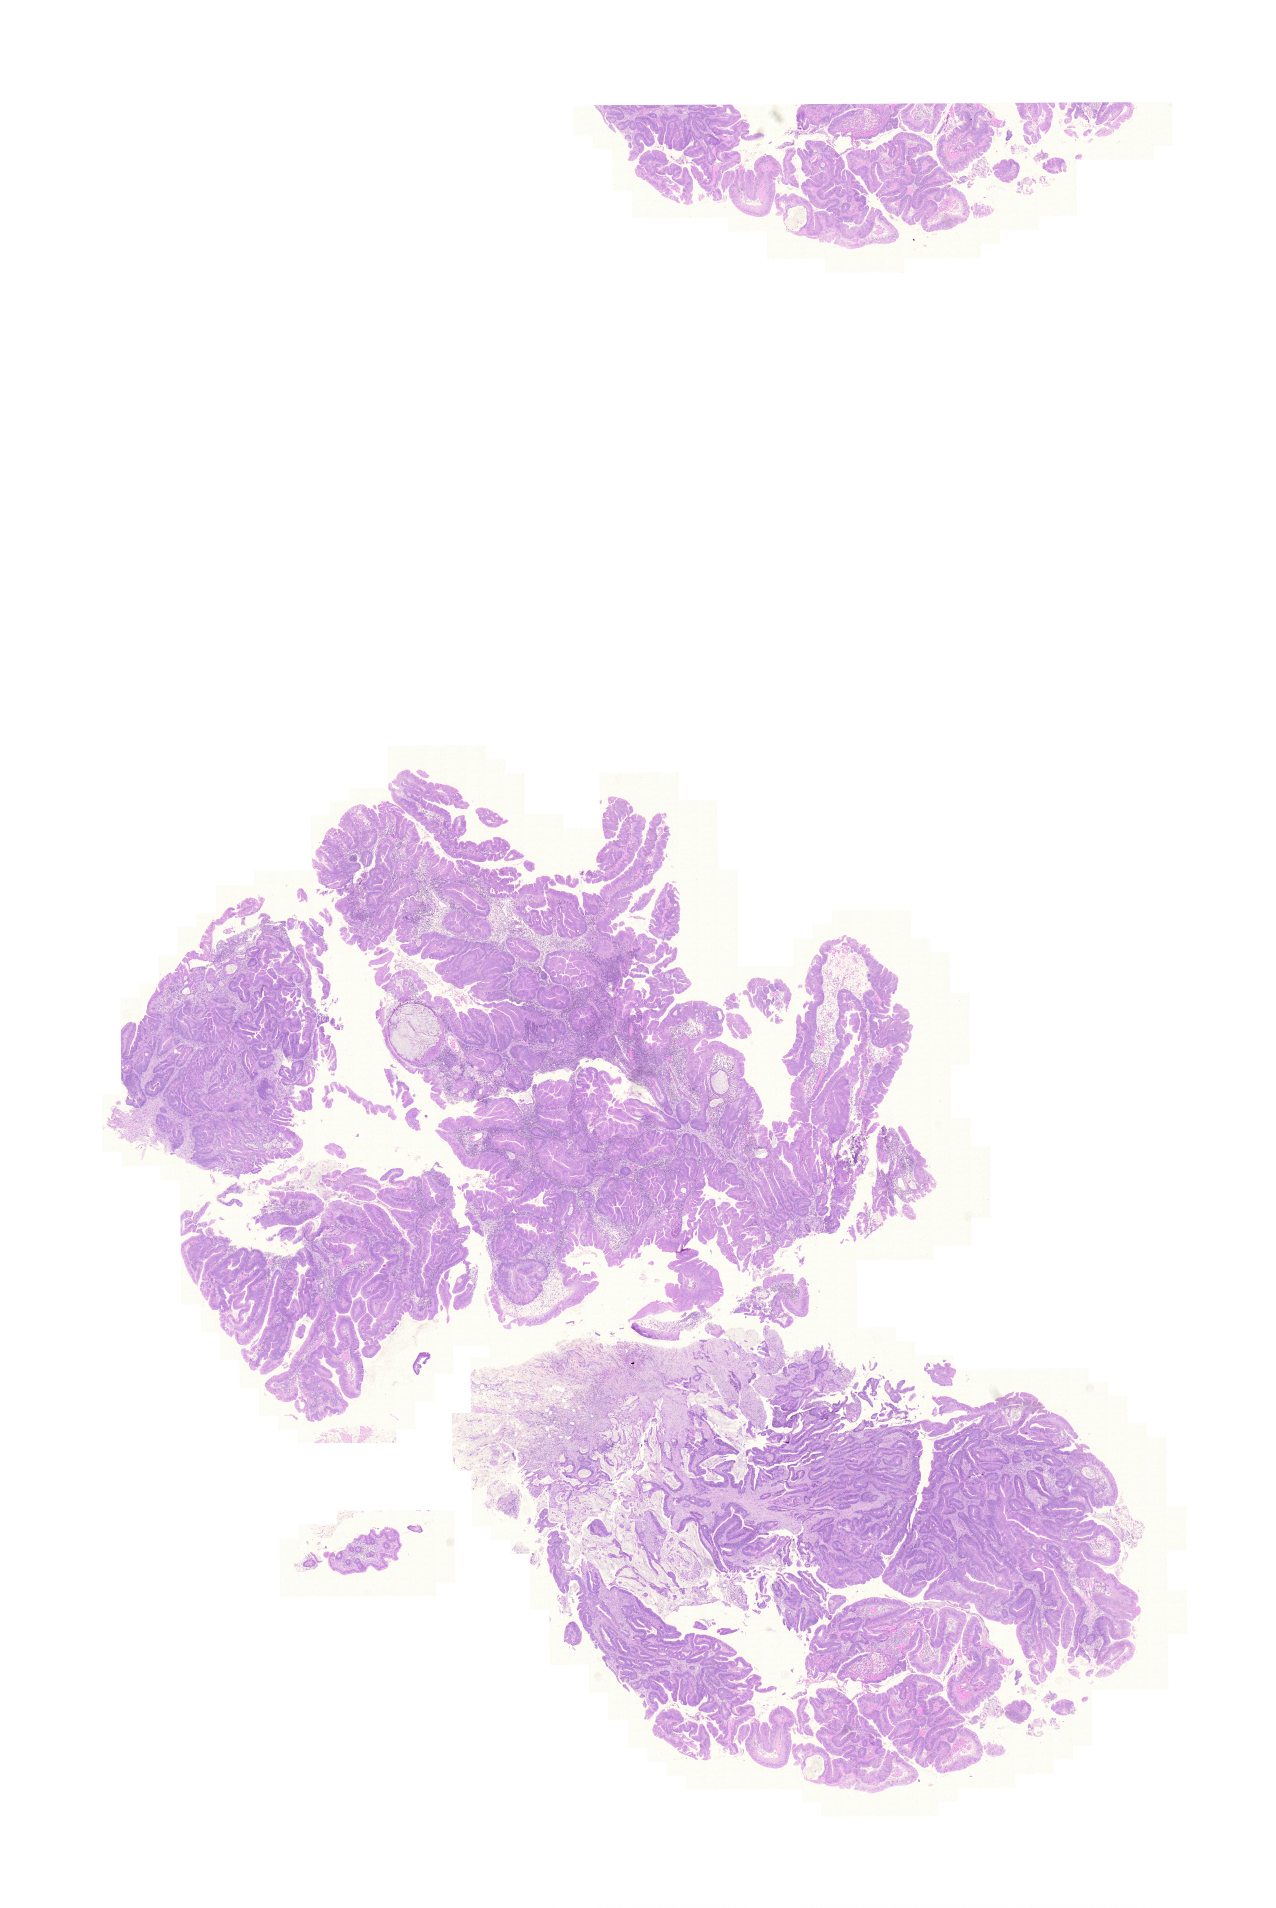
Digitized H&E tissue section (whole slide), whole scanned area (about 19.0 x 28.4 mm, slide scanned at 20x) shown as a low-resolution overview; formalin-fixed paraffin-embedded (FFPE) diagnostic section; colon, primary tumour sample. Patient: male, age at initial diagnosis 67 years.
* lymph nodes positive (case pathology): 0 of 27 examined
* TNM: T3 N0 M0
* diagnosis: Adenocarcinoma, NOS (cecum)
* AJCC pathologic stage: II